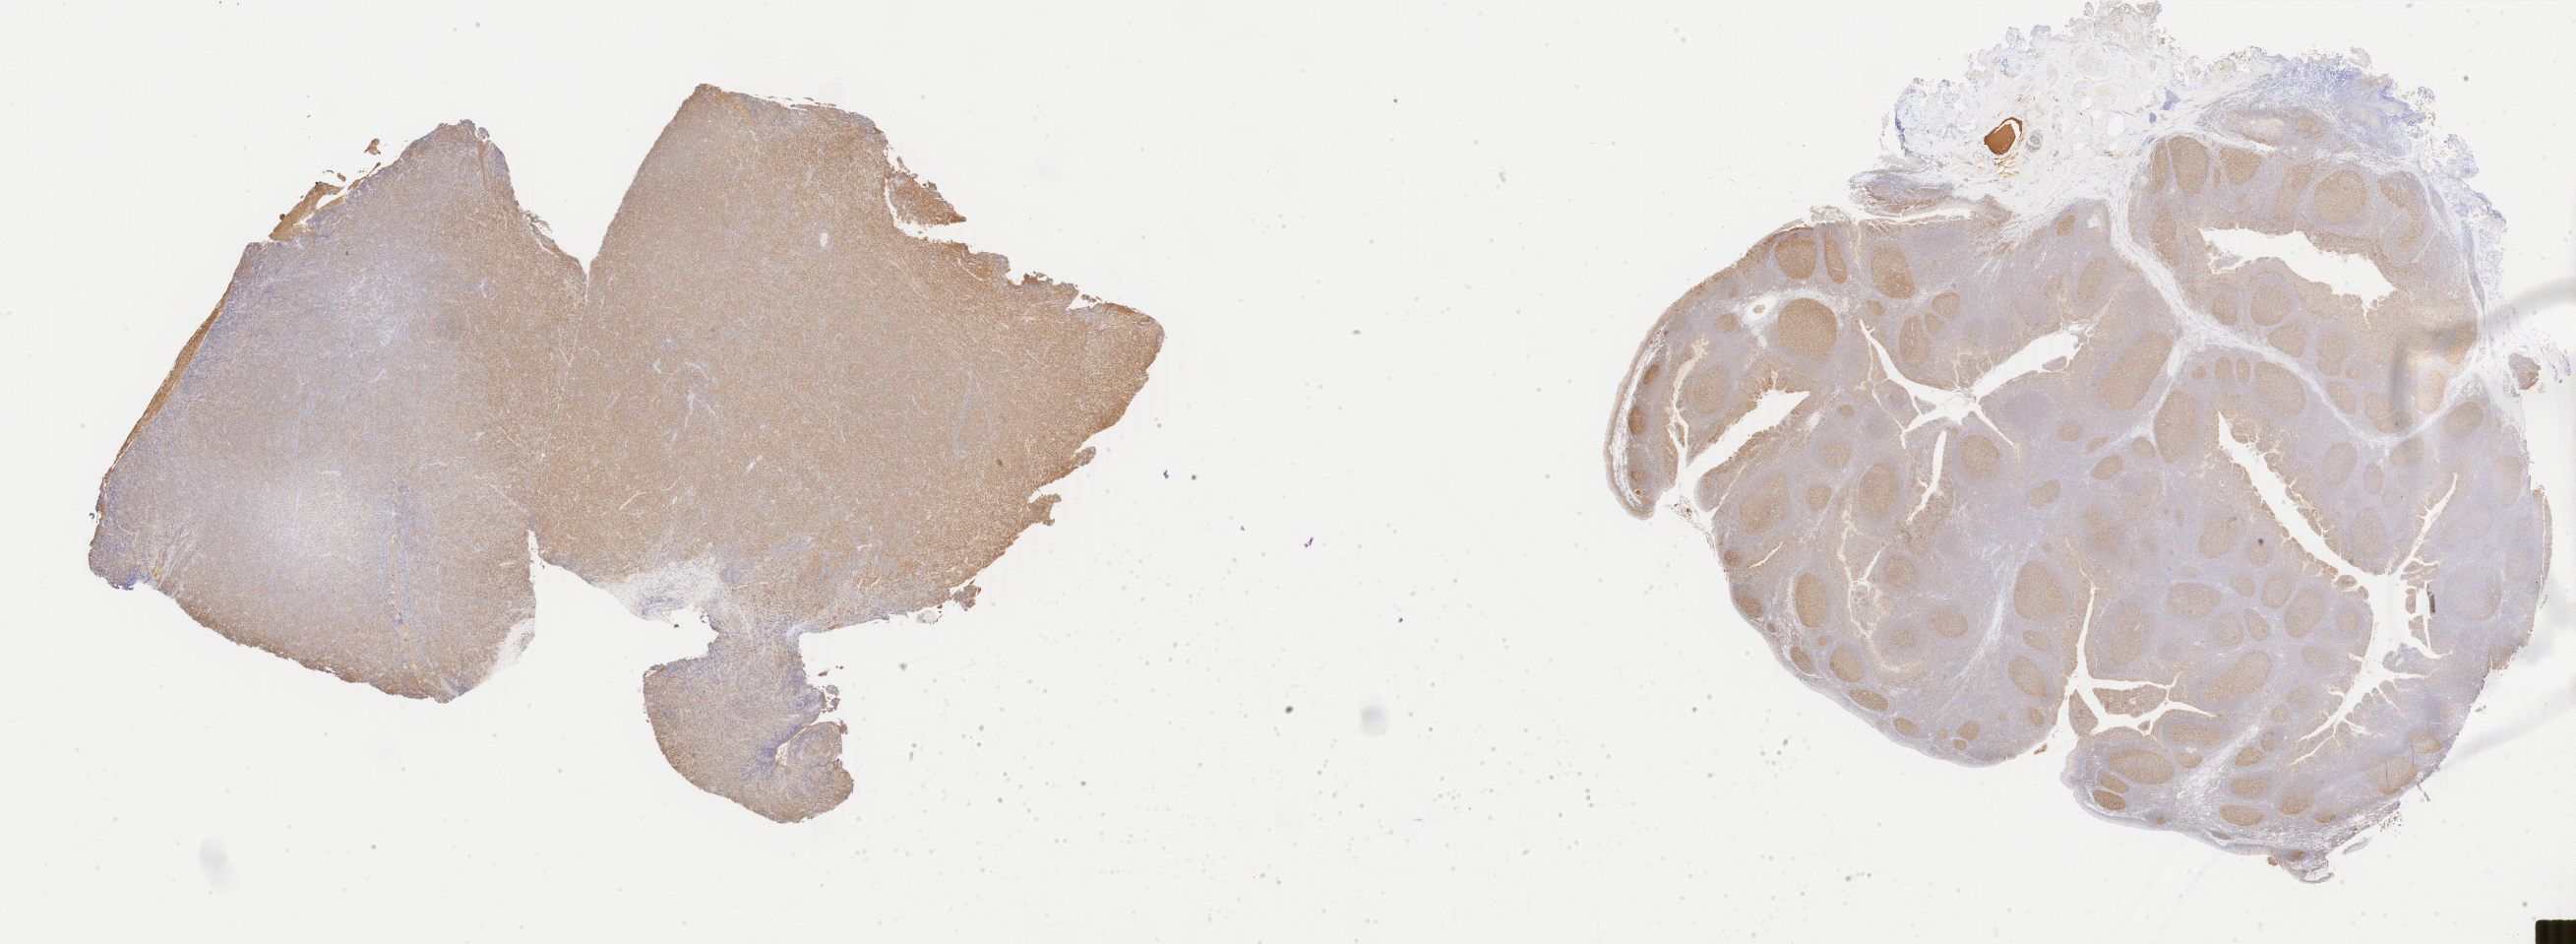
IHC for BCL6, whole-slide image, shown as a low-resolution overview of the whole scanned area (about 41.6 x 15.3 mm); specimen: tumor tissue. Male, age 7 years at initial diagnosis.
Diagnosis: Diffuse large B-cell lymphoma, NOS.